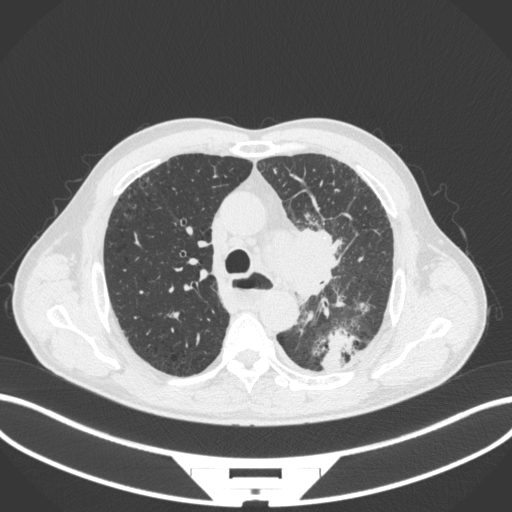
Chest CT, one axial slice. Slice 267 of 411 in the series (ordered by position). 120 kVp. Lung window (W 1500 / L -600 HU). 1 mm slice thickness. 512 × 512 image matrix, field of view 400 × 400 mm. Male patient, age 57 years. From the clinical record (not read from this slice): clinical TNM (as recorded): T2a N1 M0.
Outlined on this slice (bounding box drawn by a radiologist):
- lung tumour (recorded histology: squamous cell carcinoma): bounding box [x1, y1, x2, y2] px = [262, 217, 348, 302]